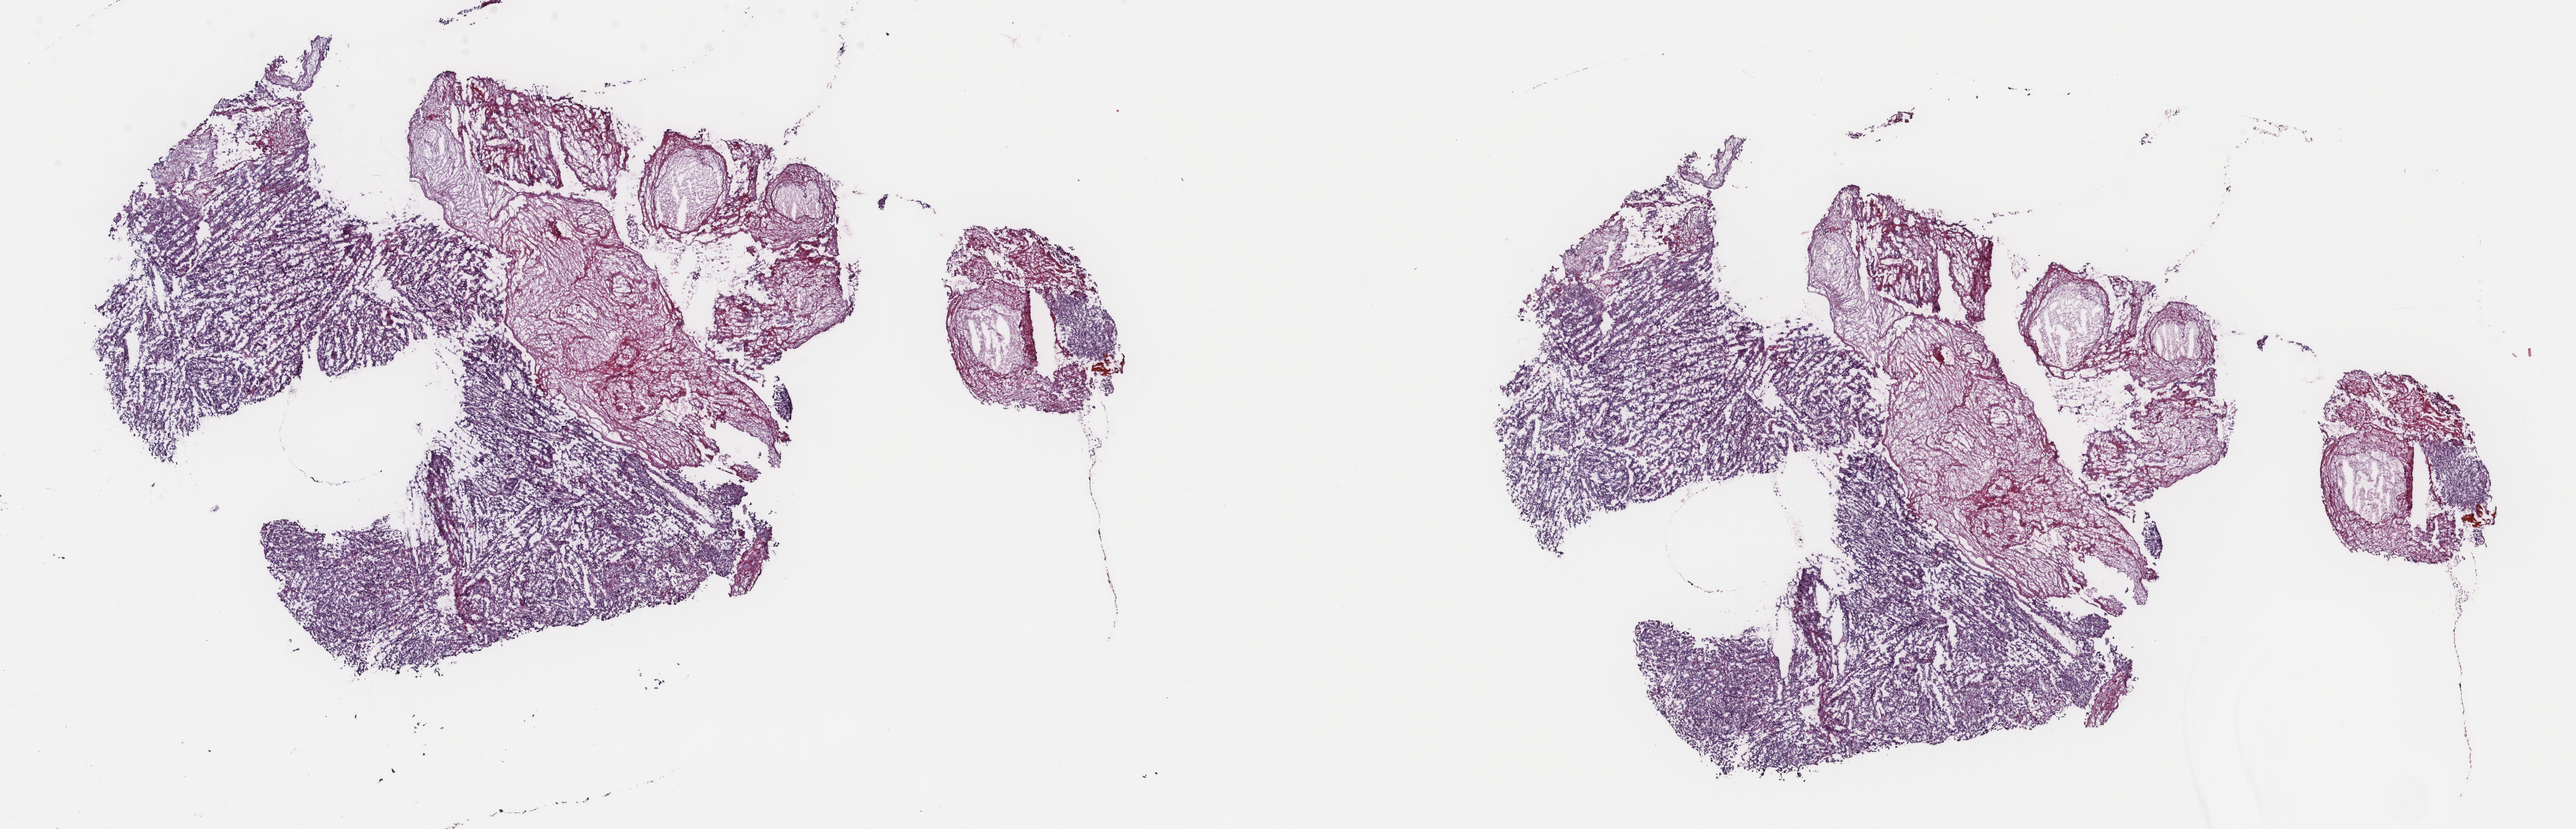
Whole-slide histology image, Hematoxylin and eosin (H&E) stained, a low-resolution overview of the entire scanned area, about 26.0 x 8.4 mm (from a 40x scan). Frozen section from the top of the tissue portion. Uterus, primary tumour sample. Female patient; age at initial diagnosis 66 years.
Histologic diagnosis: Serous cystadenocarcinoma, NOS.